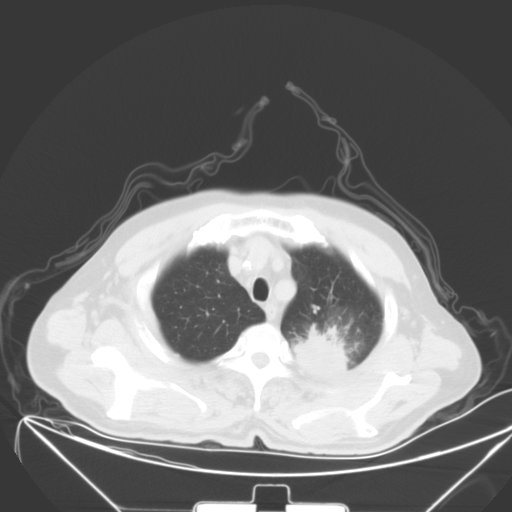
Chest CT, one axial slice; slice 50 of 64 in the series (ordered by position); 120 kVp; lung window (W 1500 / L -600 HU); 5 mm slice thickness; 512 × 512 image matrix, field of view 431 × 431 mm. Patient: male, 58 years. From the clinical record (not read from this slice): clinical TNM (as recorded): T2b N3 M1b.
Annotated regions visible in this slice (bounding box drawn by a radiologist):
- lung tumour (recorded histology: adenocarcinoma): box from (x=293, y=318) to (x=348, y=384) px